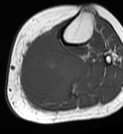
MRI of an extremity soft-tissue mass, one axial slice. Position 34 of 68 along the scan axis. MR volume resampled by the dataset authors to the PET/CT grid (not the native acquisition matrix). 3.27 mm slice thickness. 123 × 134 image matrix, field of view 120 × 131 mm. Female patient. From the clinical record (not read from this slice): histological type: extraskeletal high grade osteogenic sarcoma; grade: high; site of the primary tumour: left calf.
Structures marked on this image (expert contour drawn on MRI and transferred to this co-registered scan by the dataset authors):
- gross tumour volume (mass): bounding box (x1, y1, x2, y2) in pixels: (20, 34, 82, 99)